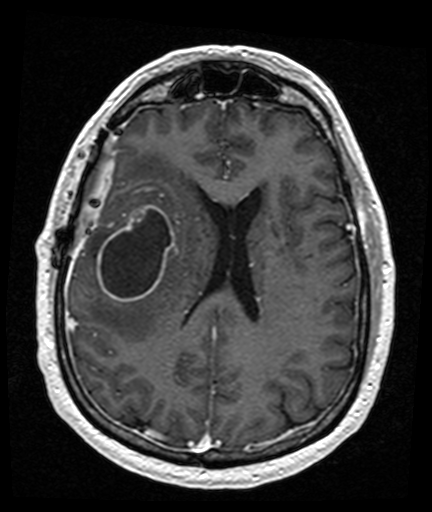
Brain MRI from a brain-tumour surgery series, one axial slice; slice 65 of 176 in the series (ordered by position); T1-weighted post-contrast; 1 mm slice thickness; 432 × 512 image matrix, field of view 194 × 230 mm. Case-level facts recorded for this patient, not image findings: histopathology: Glioblastoma; WHO grade: 4; IDH mutation: no.
Outlined on this slice (expert manual segmentation):
- tumour: bounding box [x1, y1, x2, y2] px = [97, 205, 175, 302]